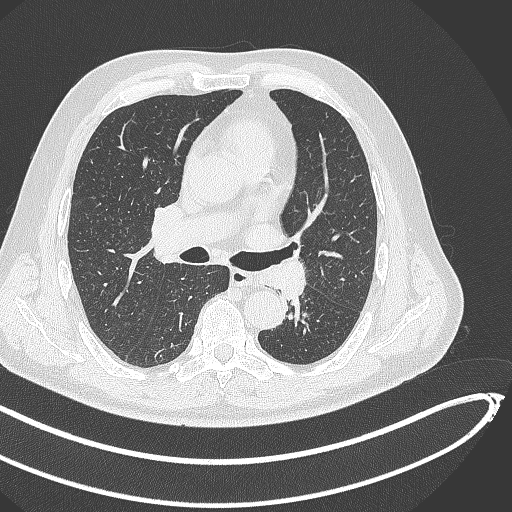
Chest CT, one axial slice. Slice 271 of 468 in the series (ordered by position). Reconstruction kernel B70f. Lung window (W 1500 / L -600 HU). 1 mm slice thickness. 512 × 512 image matrix. Patient: male, 64 years. Case-level facts recorded for this patient, not image findings: clinical TNM (as recorded): T1c N0 M0.
Structures marked on this image (bounding box drawn by a radiologist):
- lung tumour (recorded histology: squamous cell carcinoma): bounding box <258,255,315,298> (left, top, right, bottom; pixels)